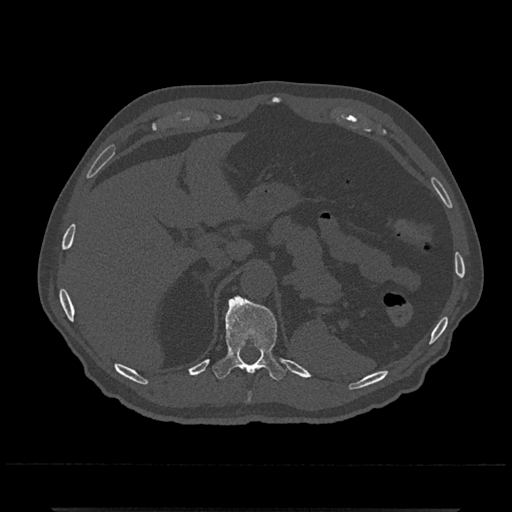
CT including the spine, one axial slice. Position 499 of 797 along the scan axis. 120 kVp. Bone window (W 1800 / L 400 HU). 0.5 mm slice thickness. 512 × 512 image matrix, field of view 393 × 393 mm. Male patient, age 67 years. From the clinical record (not read from this slice): primary cancer: prostate.
Outlined on this slice (semi-automatic segmentation, software-assisted and operator-edited):
- T10 vertebra: box from (x=247, y=392) to (x=252, y=402) px
- T11 vertebra: (x=212, y=295)–(x=287, y=382)